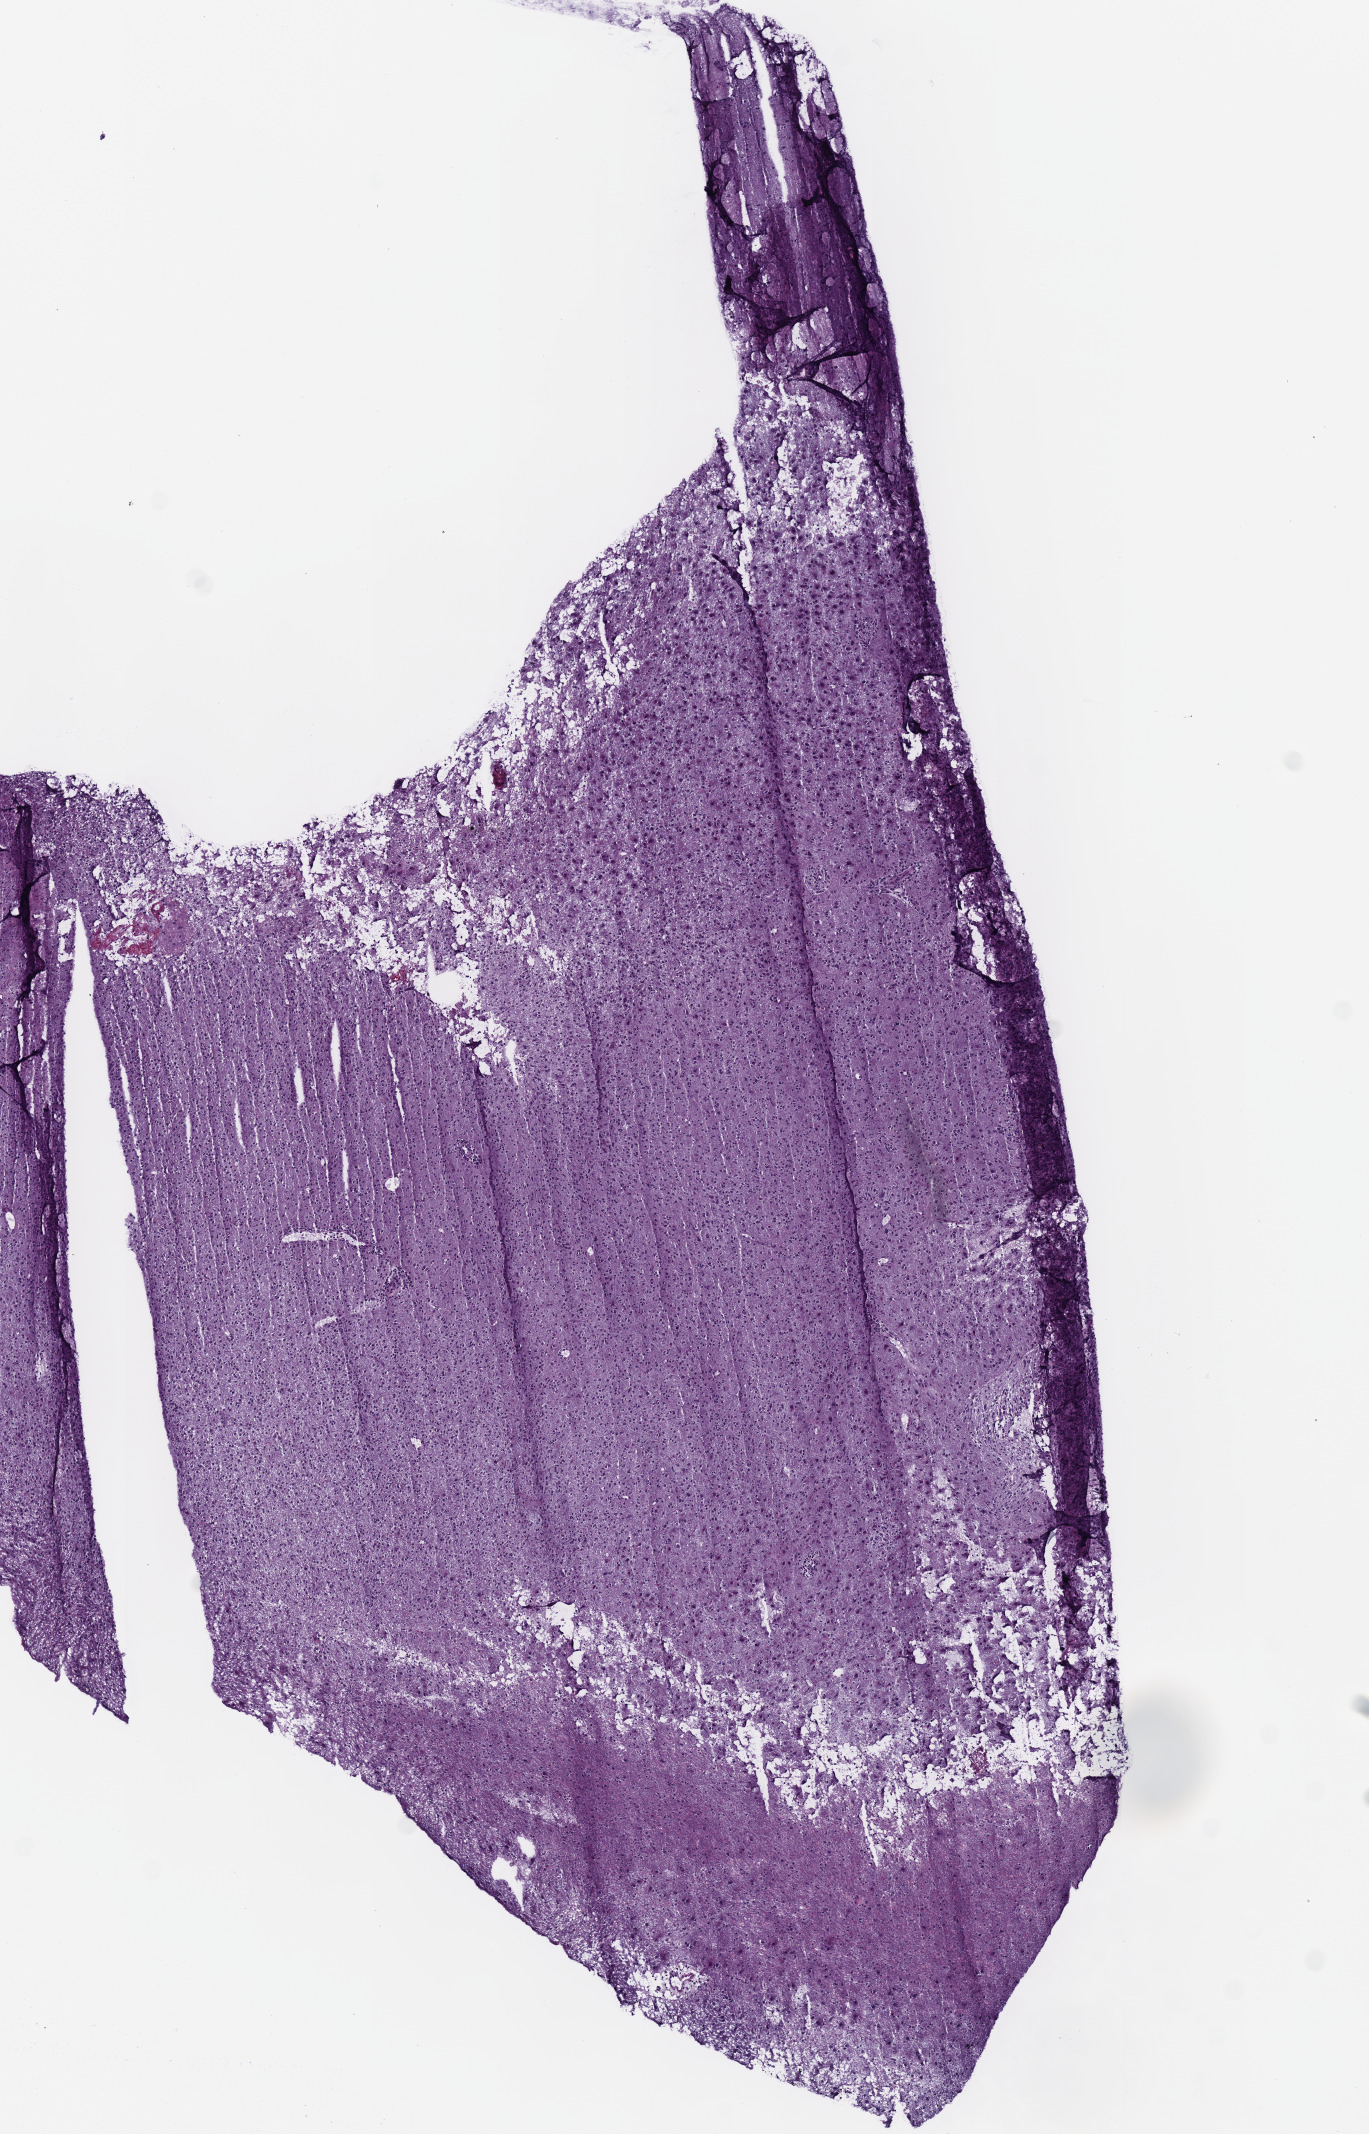
Whole-slide histology image, H&E — shown as a low-resolution overview of the whole scanned area (about 5.4 x 8.4 mm, slide scanned at 40x); frozen section; primary tumour sample from the brain. Patient: female, age at initial diagnosis 63 years. Histologic grade: G3 (poorly differentiated). Slide review estimates, as recorded: tumour cells 100%, tumour nuclei 75%, normal cells 0%, stromal cells 0%, necrosis 0%.
Laterality: left. Diagnosis: Mixed glioma (cerebrum).